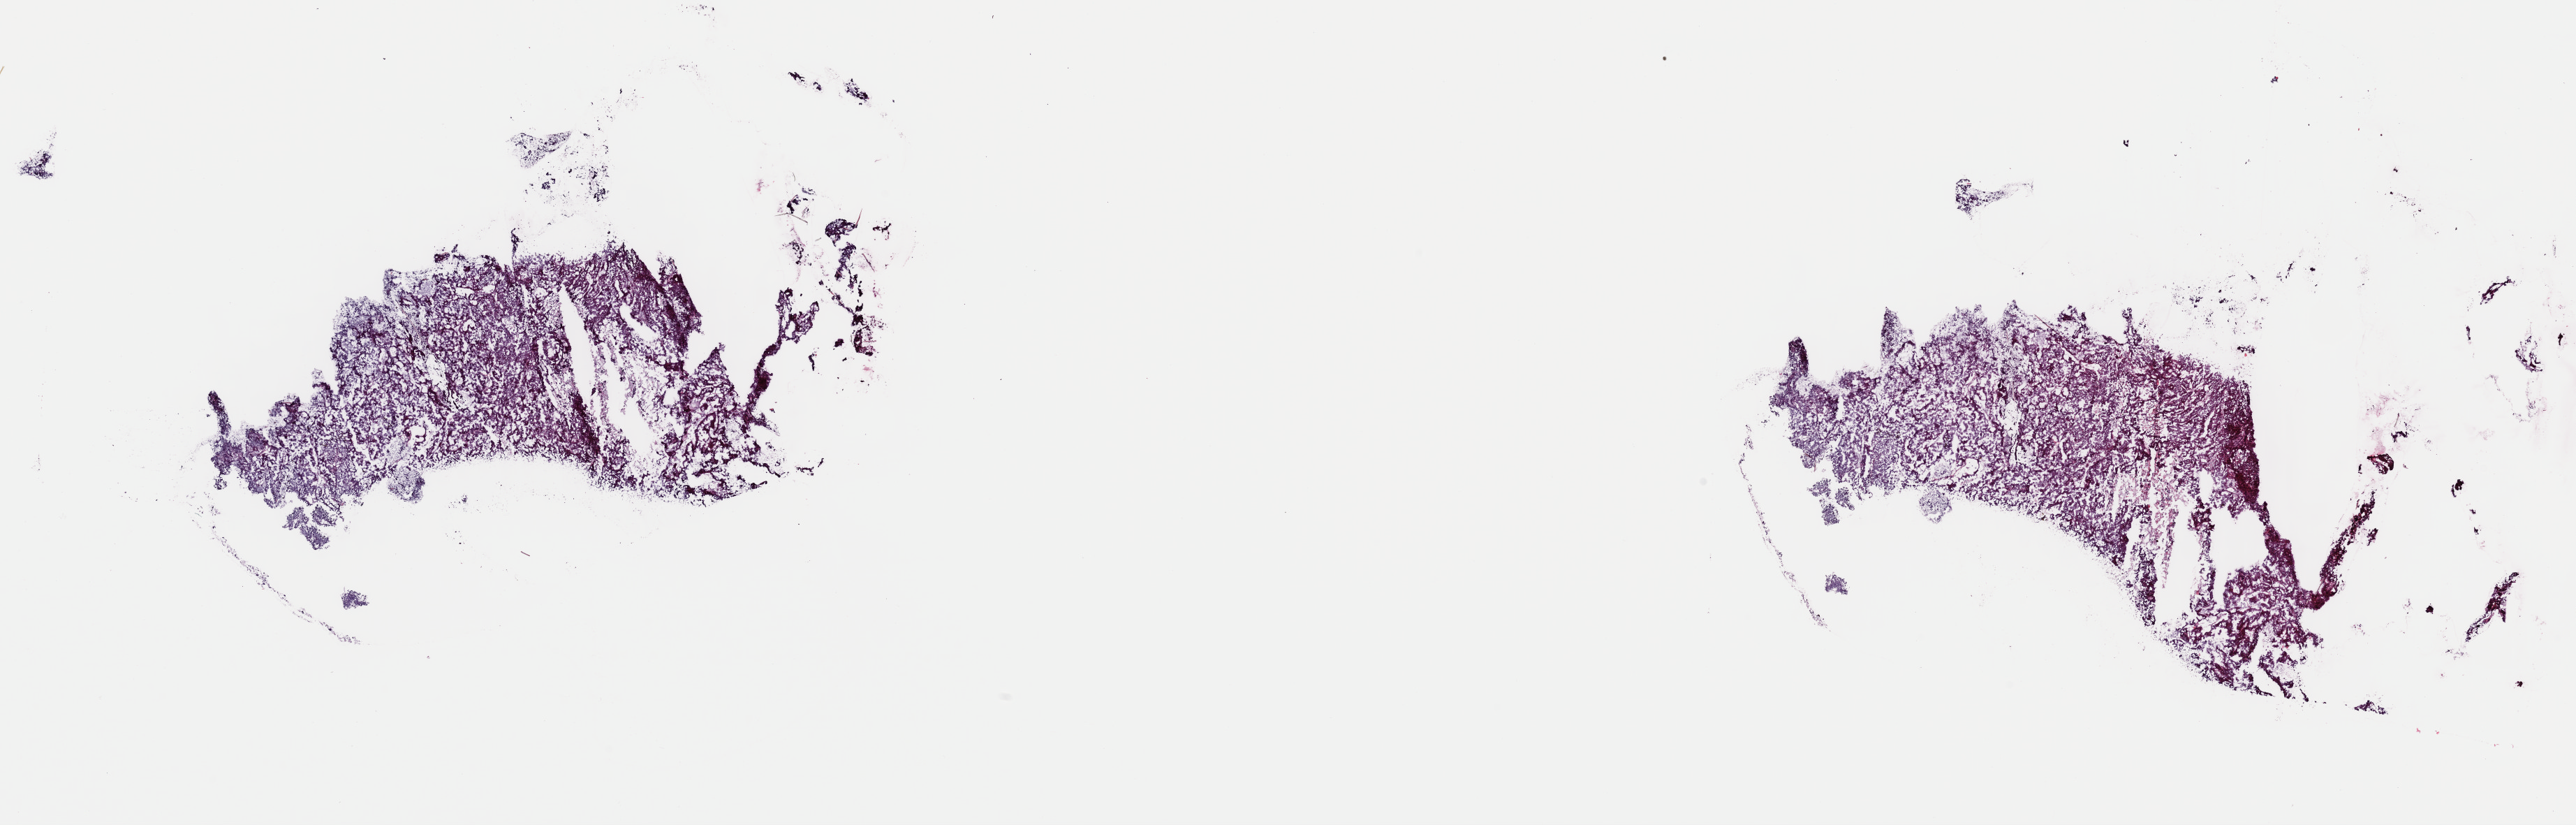
Digitized H&E-stained tissue section (whole slide) — whole scanned area (about 29.1 x 9.3 mm) shown as a low-resolution overview, frozen section from the top of the tissue portion, kidney, primary tumour sample. Patient: female, age at initial diagnosis 77 years. Composition of this section per pathologist review: tumour cells 60%, tumour nuclei 80%, normal cells 0%, stromal cells 20%, necrosis 20%. Infiltration values recorded for this section: lymphocyte infiltration 5%, monocyte infiltration 5%, neutrophil infiltration 0%.
- AJCC pathologic stage: I (7th edition)
- pathologic diagnosis: Papillary adenocarcinoma, NOS
- laterality: left
- TNM: T1a N0 M0